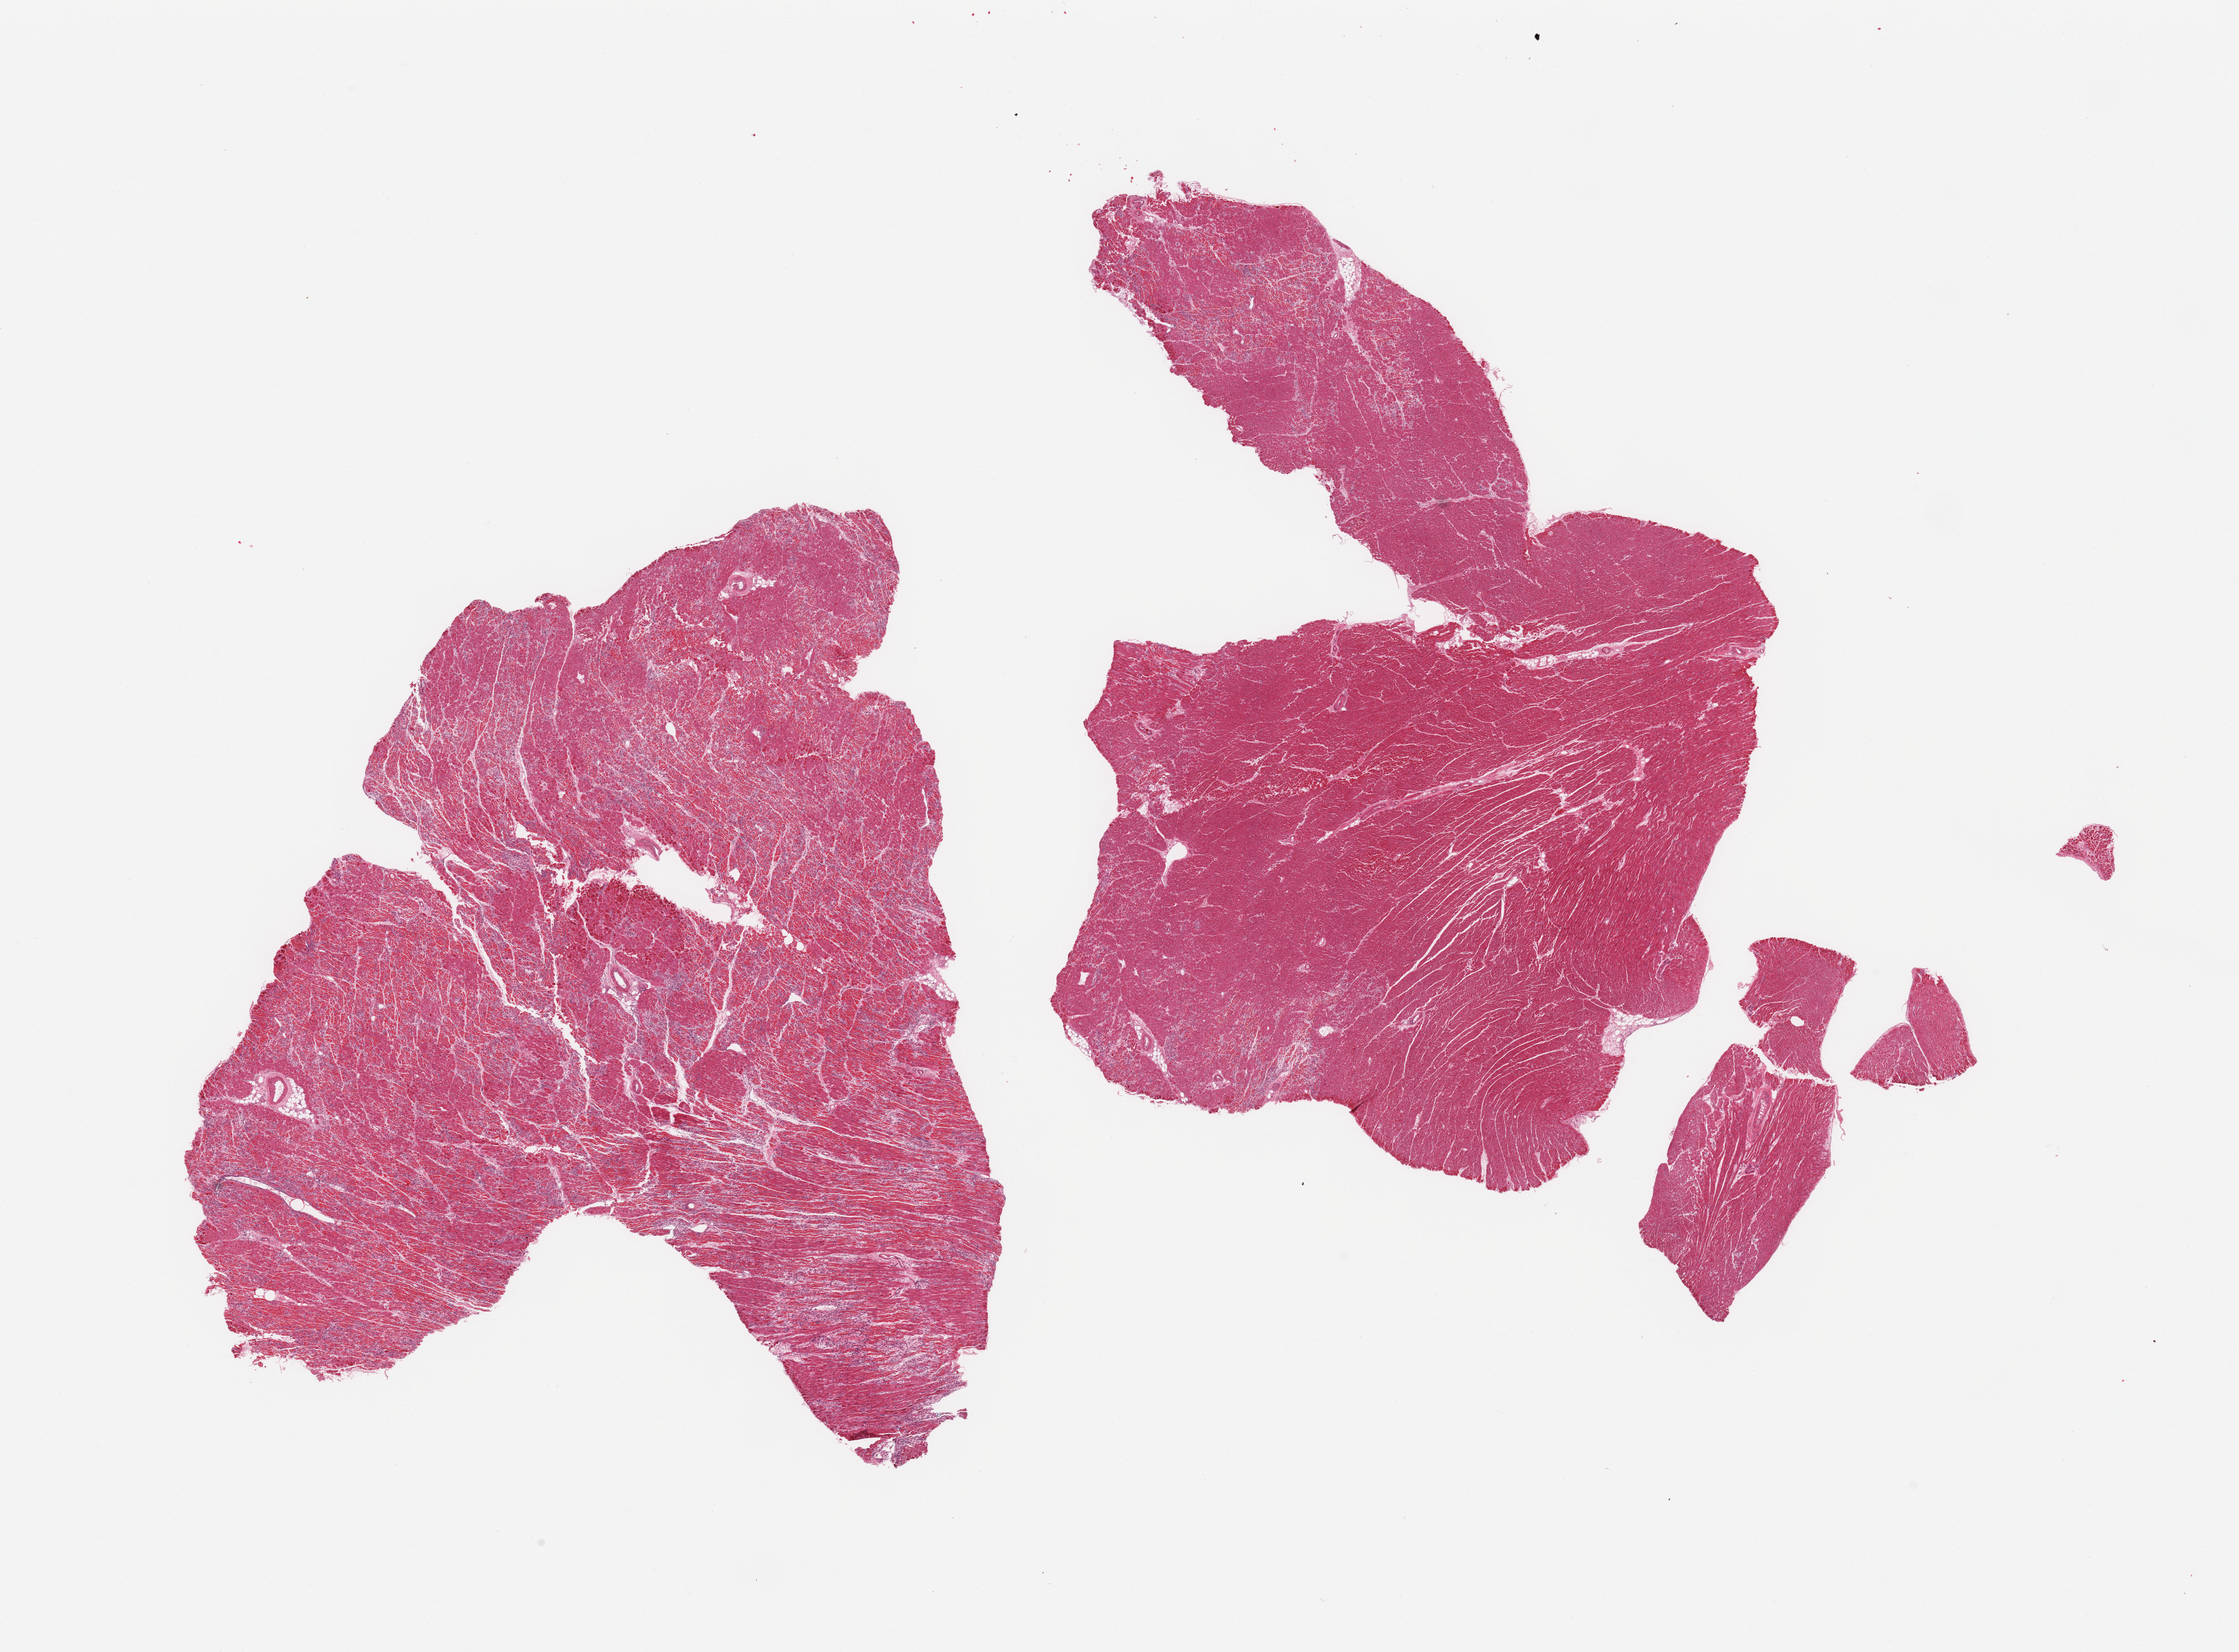
Whole-slide image, haematoxylin and eosin stain — shown as a low-resolution overview of the whole scanned area (about 26.6 x 19.6 mm). PAXgene-fixed, paraffin-embedded tissue. Section of heart (target tissue). Donor tissue sample. Donor: male.
Review note (as recorded): 2 pieces, diffuse lymphoid infiltrate with myocyte destruction c/w myocarditis.